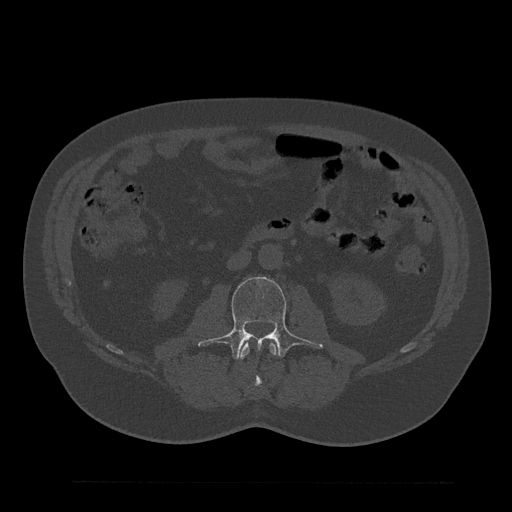
CT including the spine, one axial slice; slice 49 of 797 in the series (ordered by position); bone window (W 1800 / L 400 HU); 0.5 mm slice thickness; 512 × 512 image matrix. Patient: male, 61 years. Case-level facts recorded for this patient, not image findings: primary cancer: prostate.
Outlined on this slice (semi-automatically segmented with operator editing):
- L2 vertebra: bounding box <239,342,277,387> (left, top, right, bottom; pixels)
- L3 vertebra: <198,277,323,360>